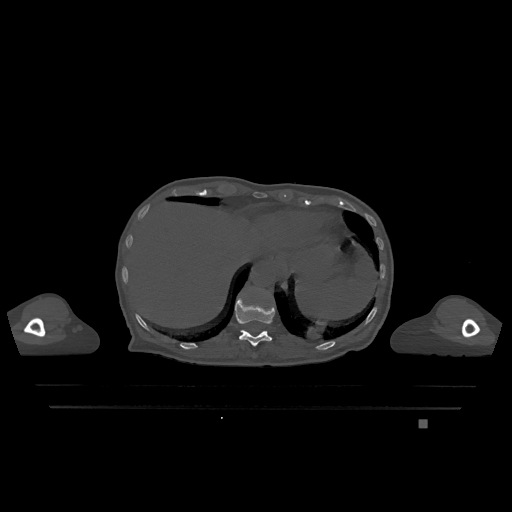
CT including the spine, one axial slice. Bone window (W 1800 / L 400 HU). 0.5 mm slice thickness. 512 × 512 image matrix. Patient: female, 74 years. Case-level facts recorded for this patient, not image findings: primary cancer: lung; vertebrae with lytic lesions (as recorded): T1, T4, T5, T6, L4, L5.
Outlined on this slice (semi-automatic segmentation, software-assisted and operator-edited):
- T11 vertebra: bounding box (x1, y1, x2, y2) in pixels: (235, 295, 275, 346)